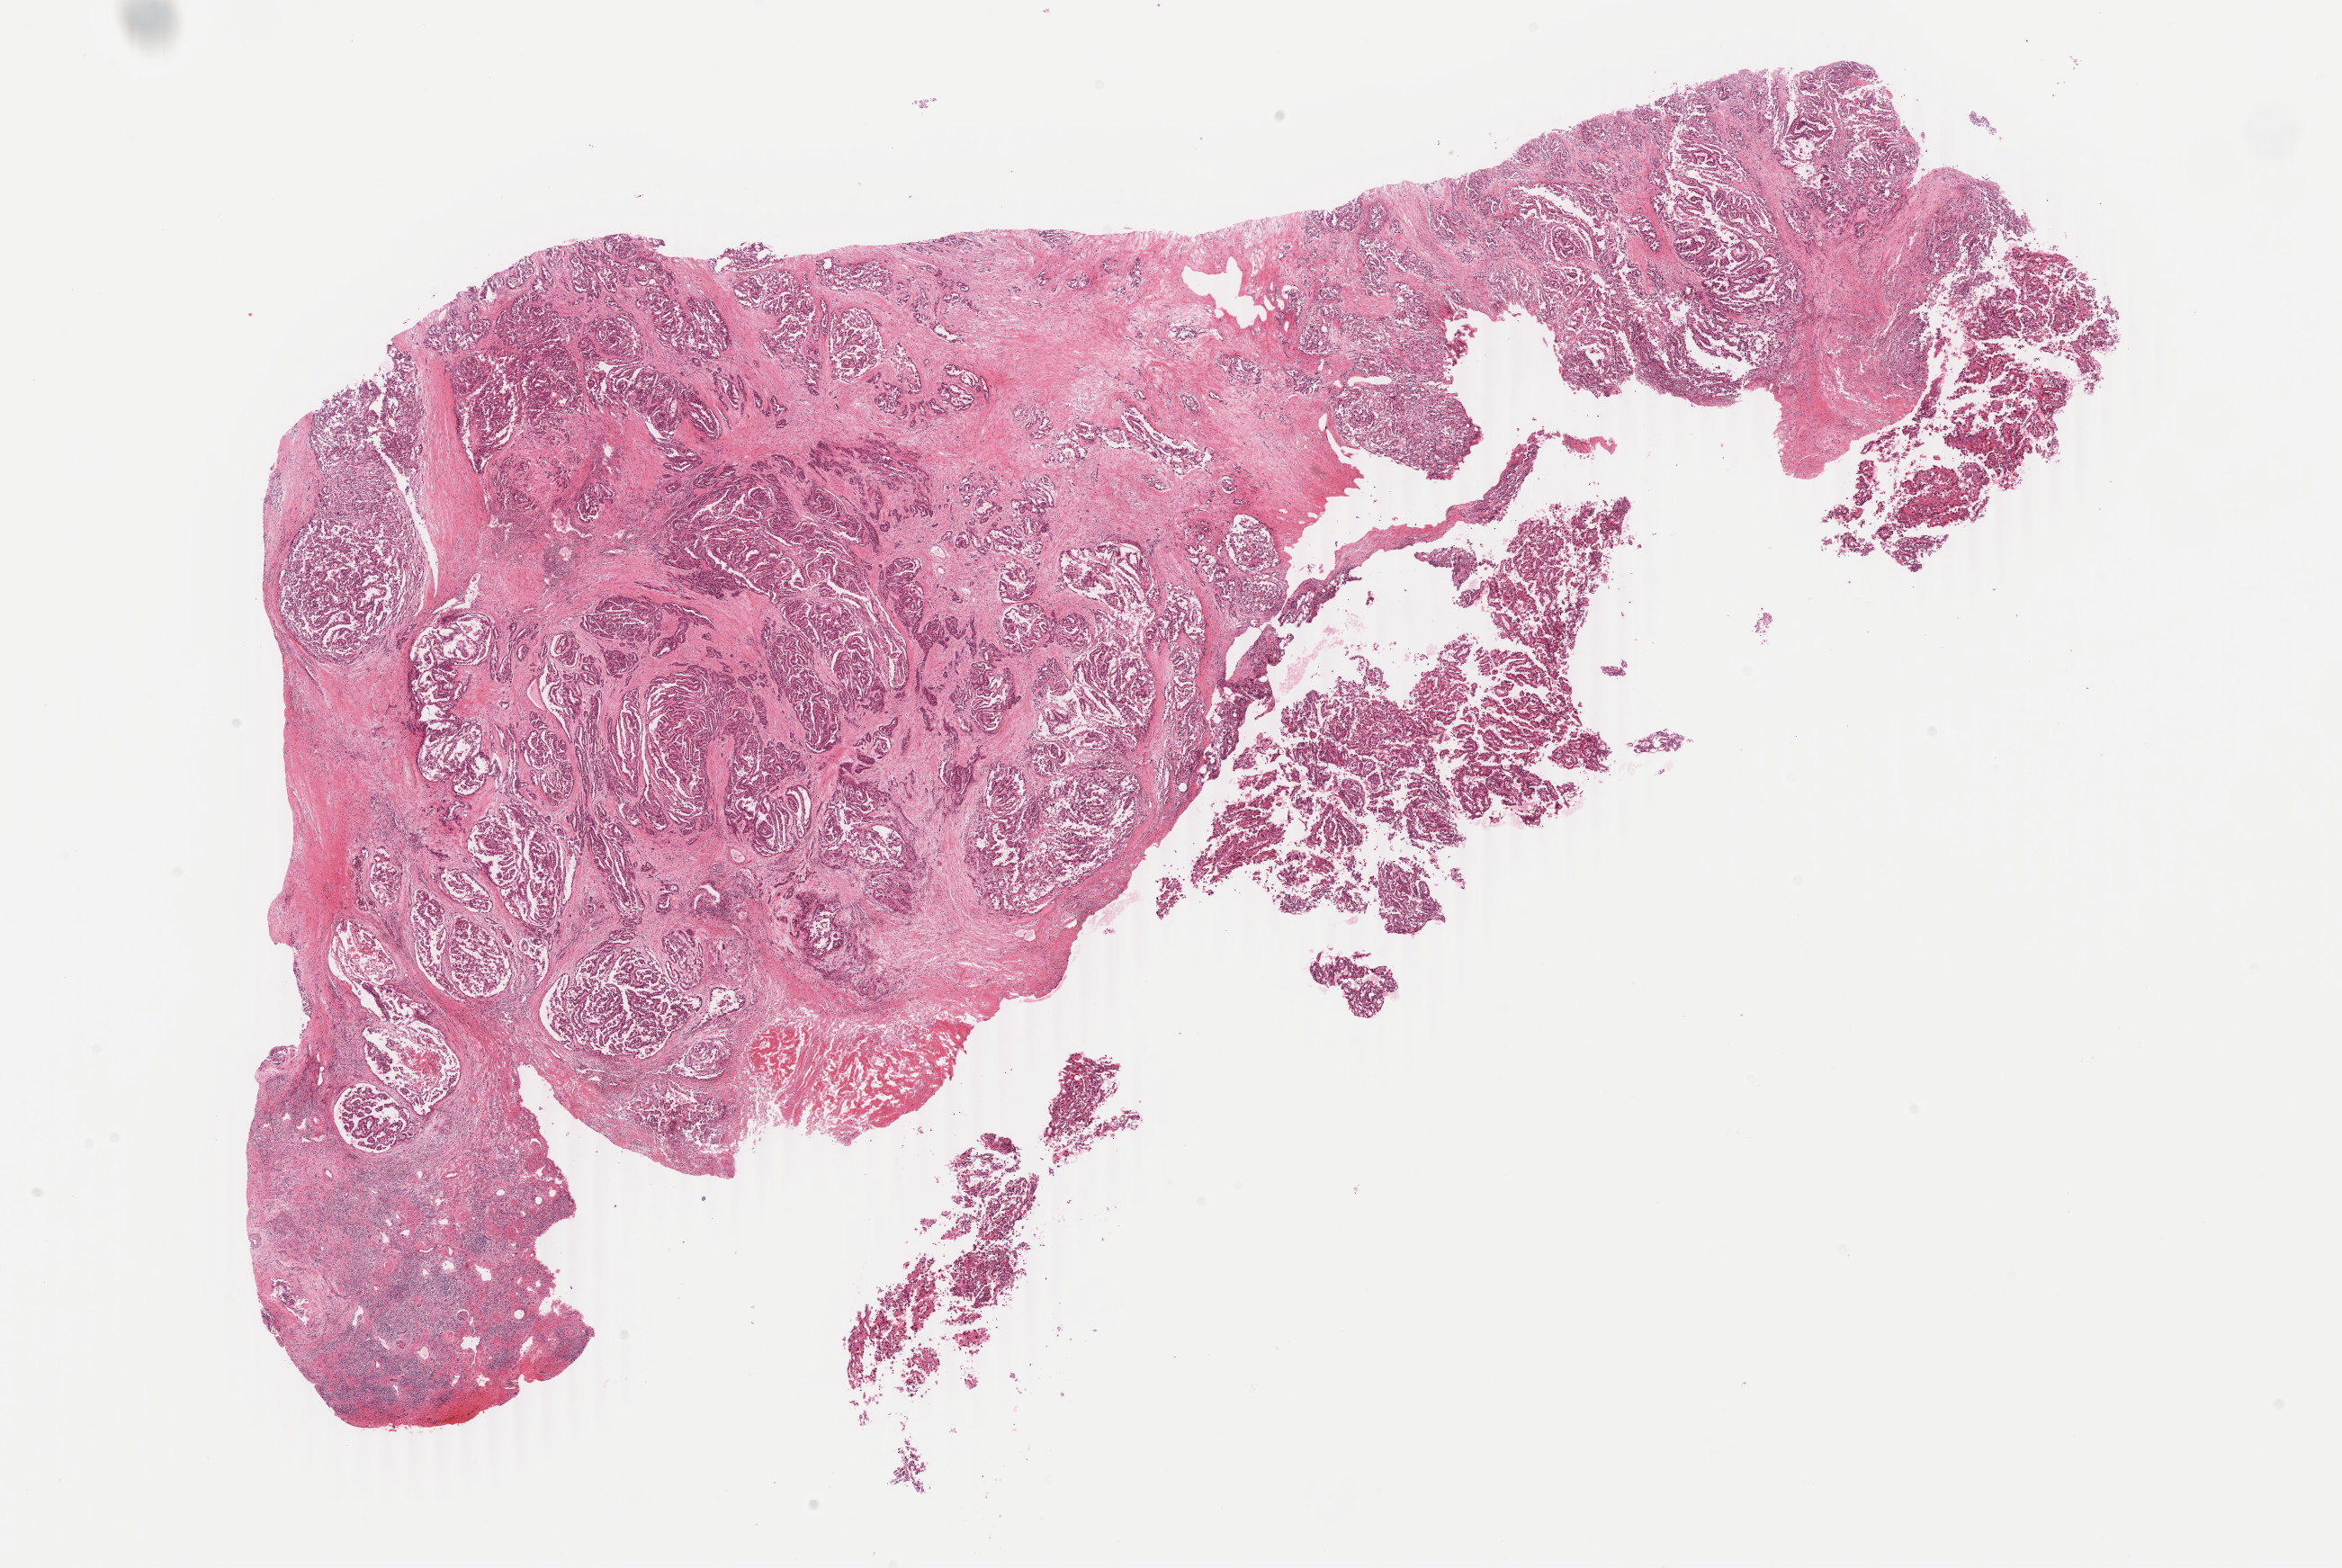
Digitized Hematoxylin and eosin (H&E) stained tissue section (whole slide) — low-resolution overview of the scanned area, about 20.7 x 13.9 mm (slide scanned at 40x); FFPE section; kidney, primary tumour sample. Male patient; age at initial diagnosis 41 years.
- diagnosis: Papillary adenocarcinoma, NOS
- AJCC pathologic stage: IV (6th edition)
- TNM: T3b N1 M1